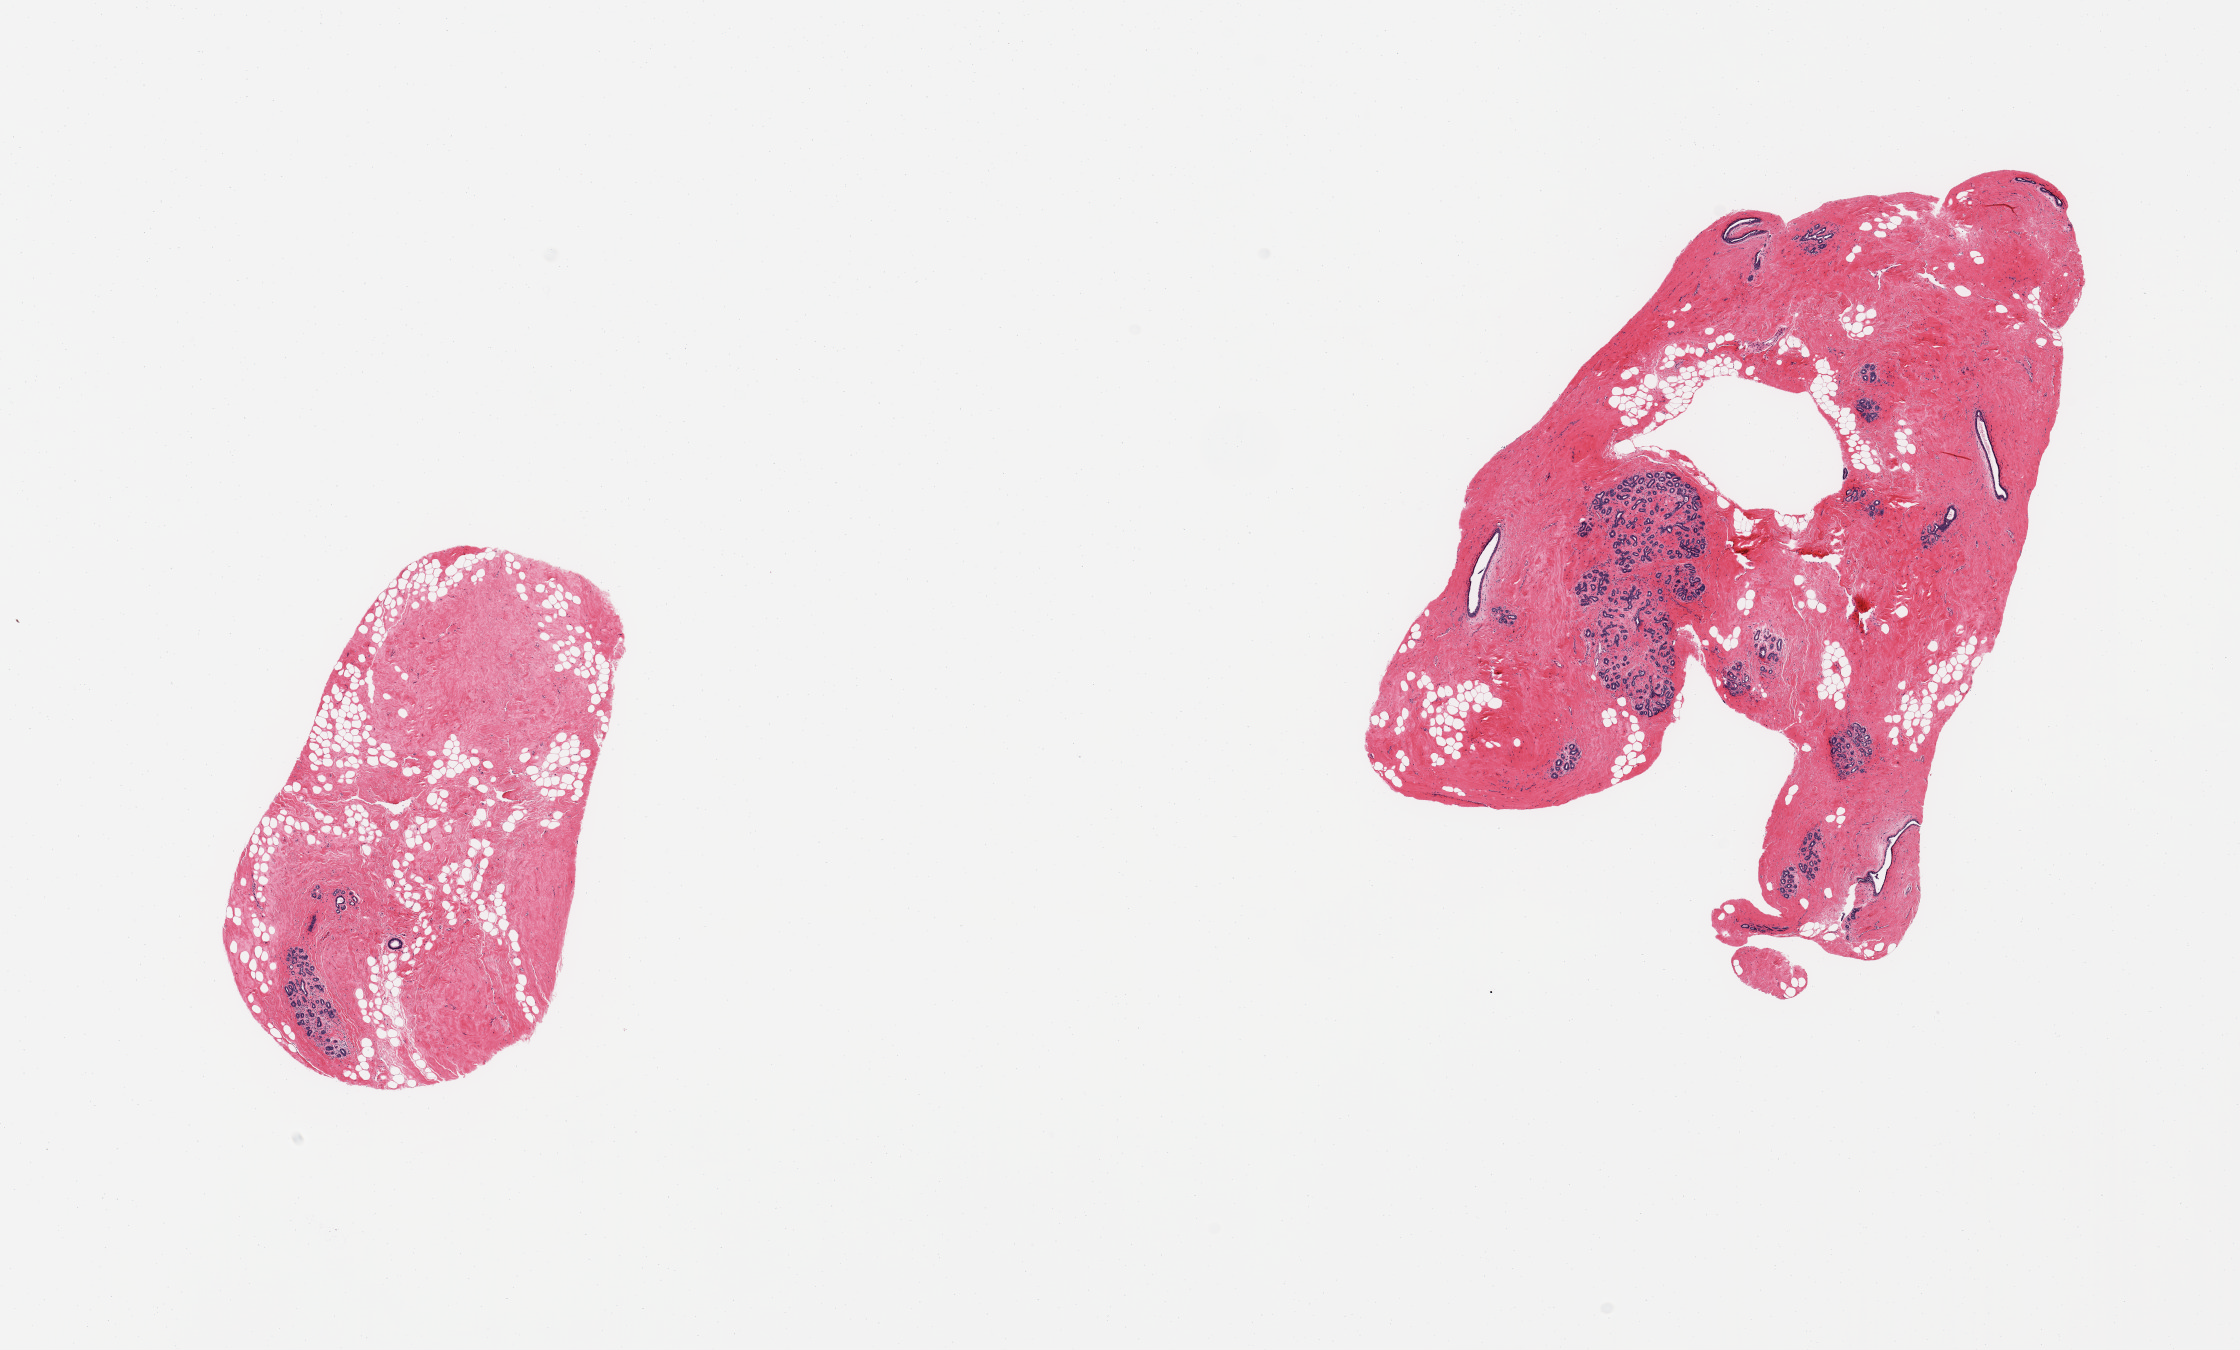
Whole-slide image, hematoxylin and eosin (H&E) stain — low-resolution overview of the scanned area, about 17.7 x 10.7 mm (from a 20x scan). PAXgene-fixed paraffin-embedded (PFPE) section. Target tissue: breast. Donor tissue sample. Donor: female.
Review note (as recorded): 2 pieces; 10-20% fat with dense fibrocollagenous stroma with embedded benign ducts and lobules.